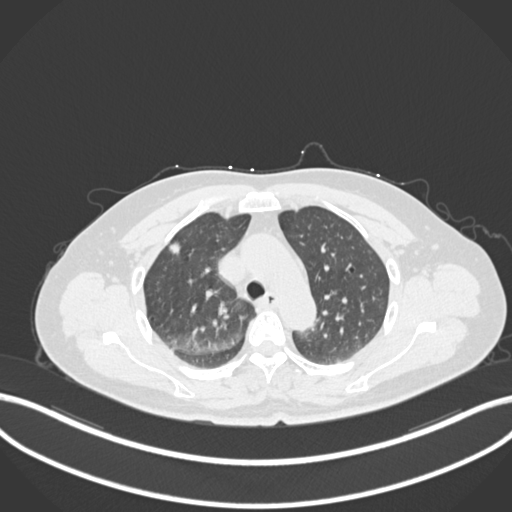
Chest CT, one axial slice; slice 167 of 223 in the series (ordered by position); lung window (W 1500 / L -600 HU); 1 mm slice thickness; 512 × 512 image matrix, field of view 400 × 400 mm. Patient: female, 56 years. Case-level facts recorded for this patient, not image findings: clinical TNM (as recorded): T1c N0 M0.
Outlined on this slice (bounding box drawn by a radiologist):
- lung tumour (recorded histology: adenocarcinoma): bounding box (x1, y1, x2, y2) in pixels: (168, 237, 186, 261)